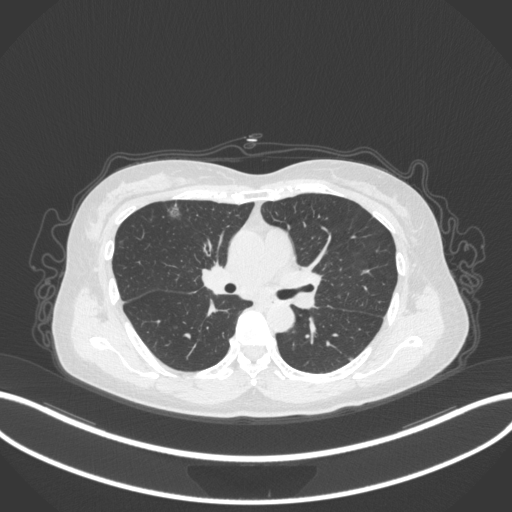
Chest CT, one axial slice. Slice 194 of 317 in the series (ordered by position). Reconstruction kernel B31f. Lung window (W 1500 / L -600 HU). 1 mm slice thickness. 512 × 512 image matrix, field of view 400 × 400 mm. Patient: female, 61 years. From the clinical record (not read from this slice): clinical TNM (as recorded): T1b N0 M0; histopathological grade: G1.
Annotated regions visible in this slice (bounding box drawn by a radiologist):
- lung tumour (recorded histology: adenocarcinoma): bounding box <162,202,183,222> (left, top, right, bottom; pixels)